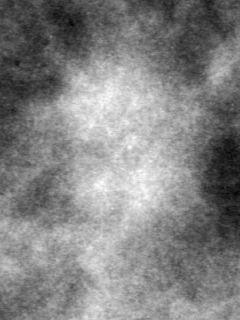
Region of interest cut from a scanned film mammogram (one marked finding); right breast; CC view.
Mass, shape irregular, margins spiculated; BI-RADS assessment category 4; subtlety rating 1 on a 1 (subtle) to 5 (obvious) scale; pathology (as recorded): malignant.